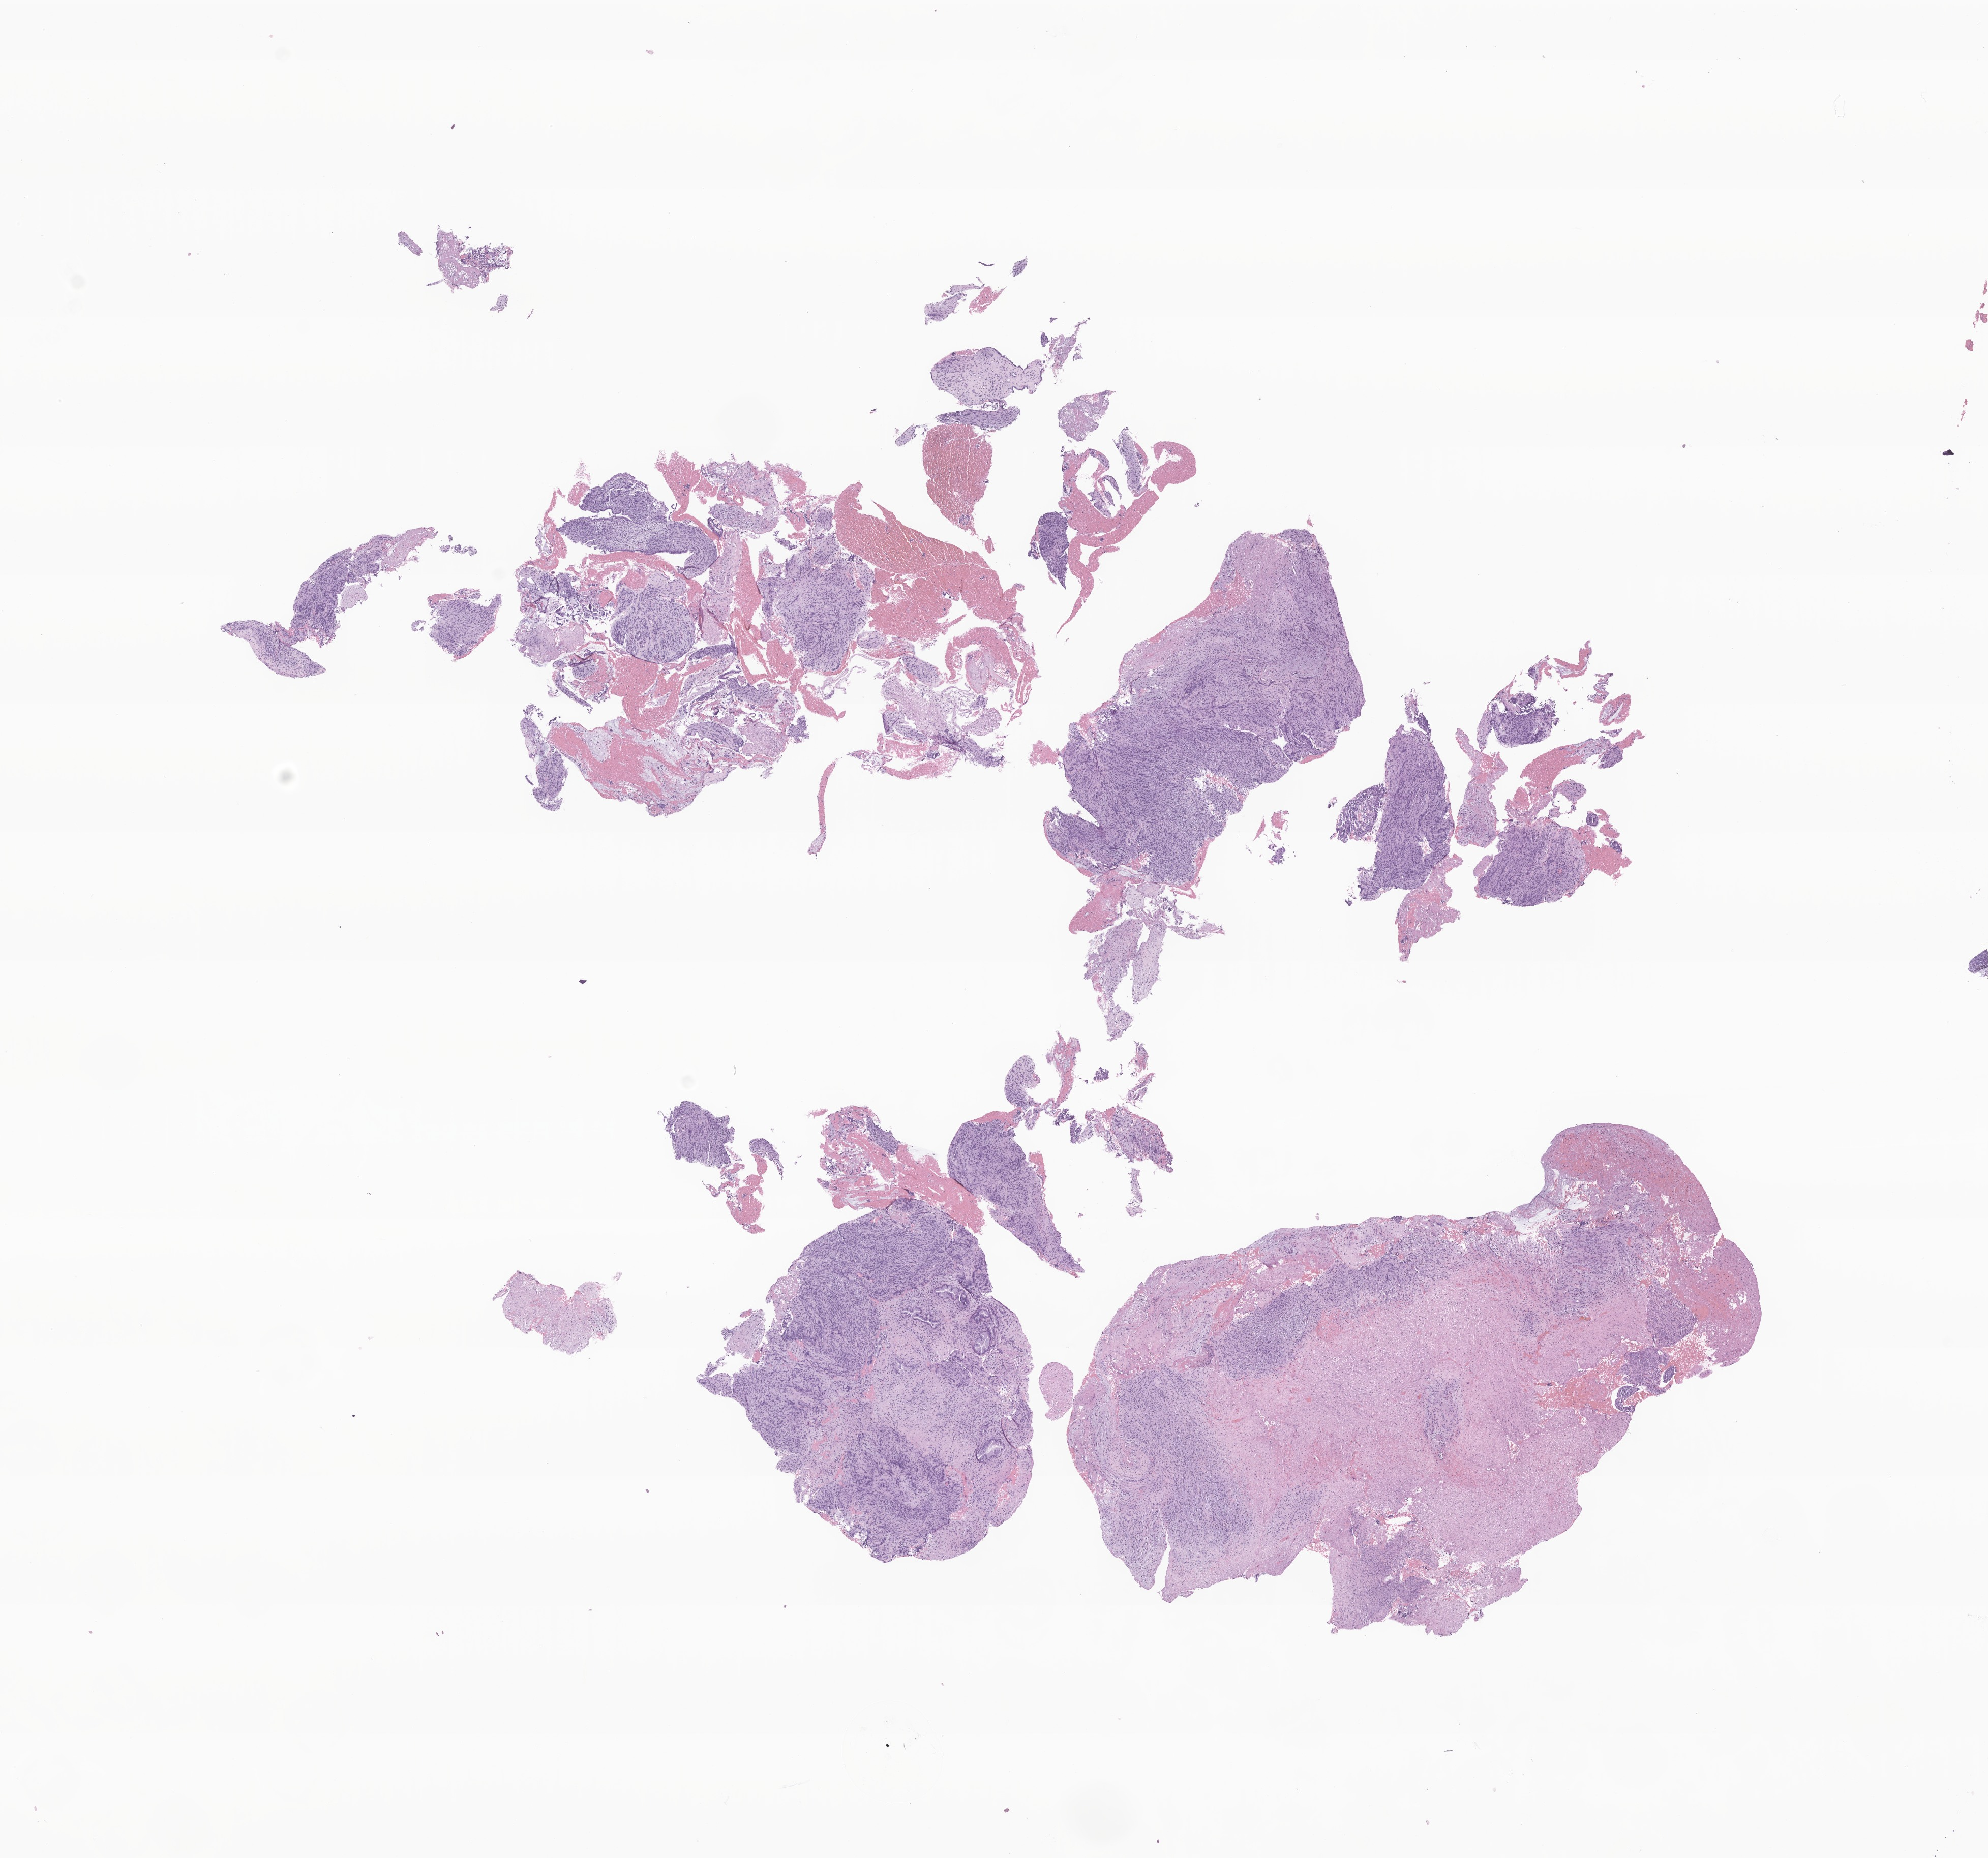
Whole-slide image, hematoxylin and eosin (H&E) stain of tumor tissue from the endocervix — low-resolution overview of the scanned area, about 16.5 x 15.4 mm, formalin-fixed paraffin-embedded section. Patient female; age 270 months (22 years 6 months).
Diagnosis (ICD-O-3 morphology term): Undifferentiated sarcoma.